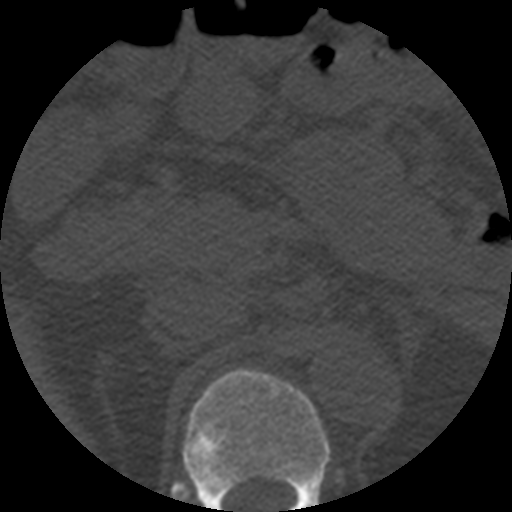
CT including the spine, one axial slice. Position 221 of 508 along the scan axis. Reconstruction kernel STANDARD. 120 kVp. Bone window (W 1800 / L 400 HU). 1.25 mm slice thickness. 512 × 512 image matrix, field of view 160 × 160 mm. Patient age 57 years. Case-level facts recorded for this patient, not image findings: primary cancer: prostate.
Outlined on this slice (semi-automatic segmentation, software-assisted and operator-edited):
- T12 vertebra: box from (x=182, y=369) to (x=331, y=512) px